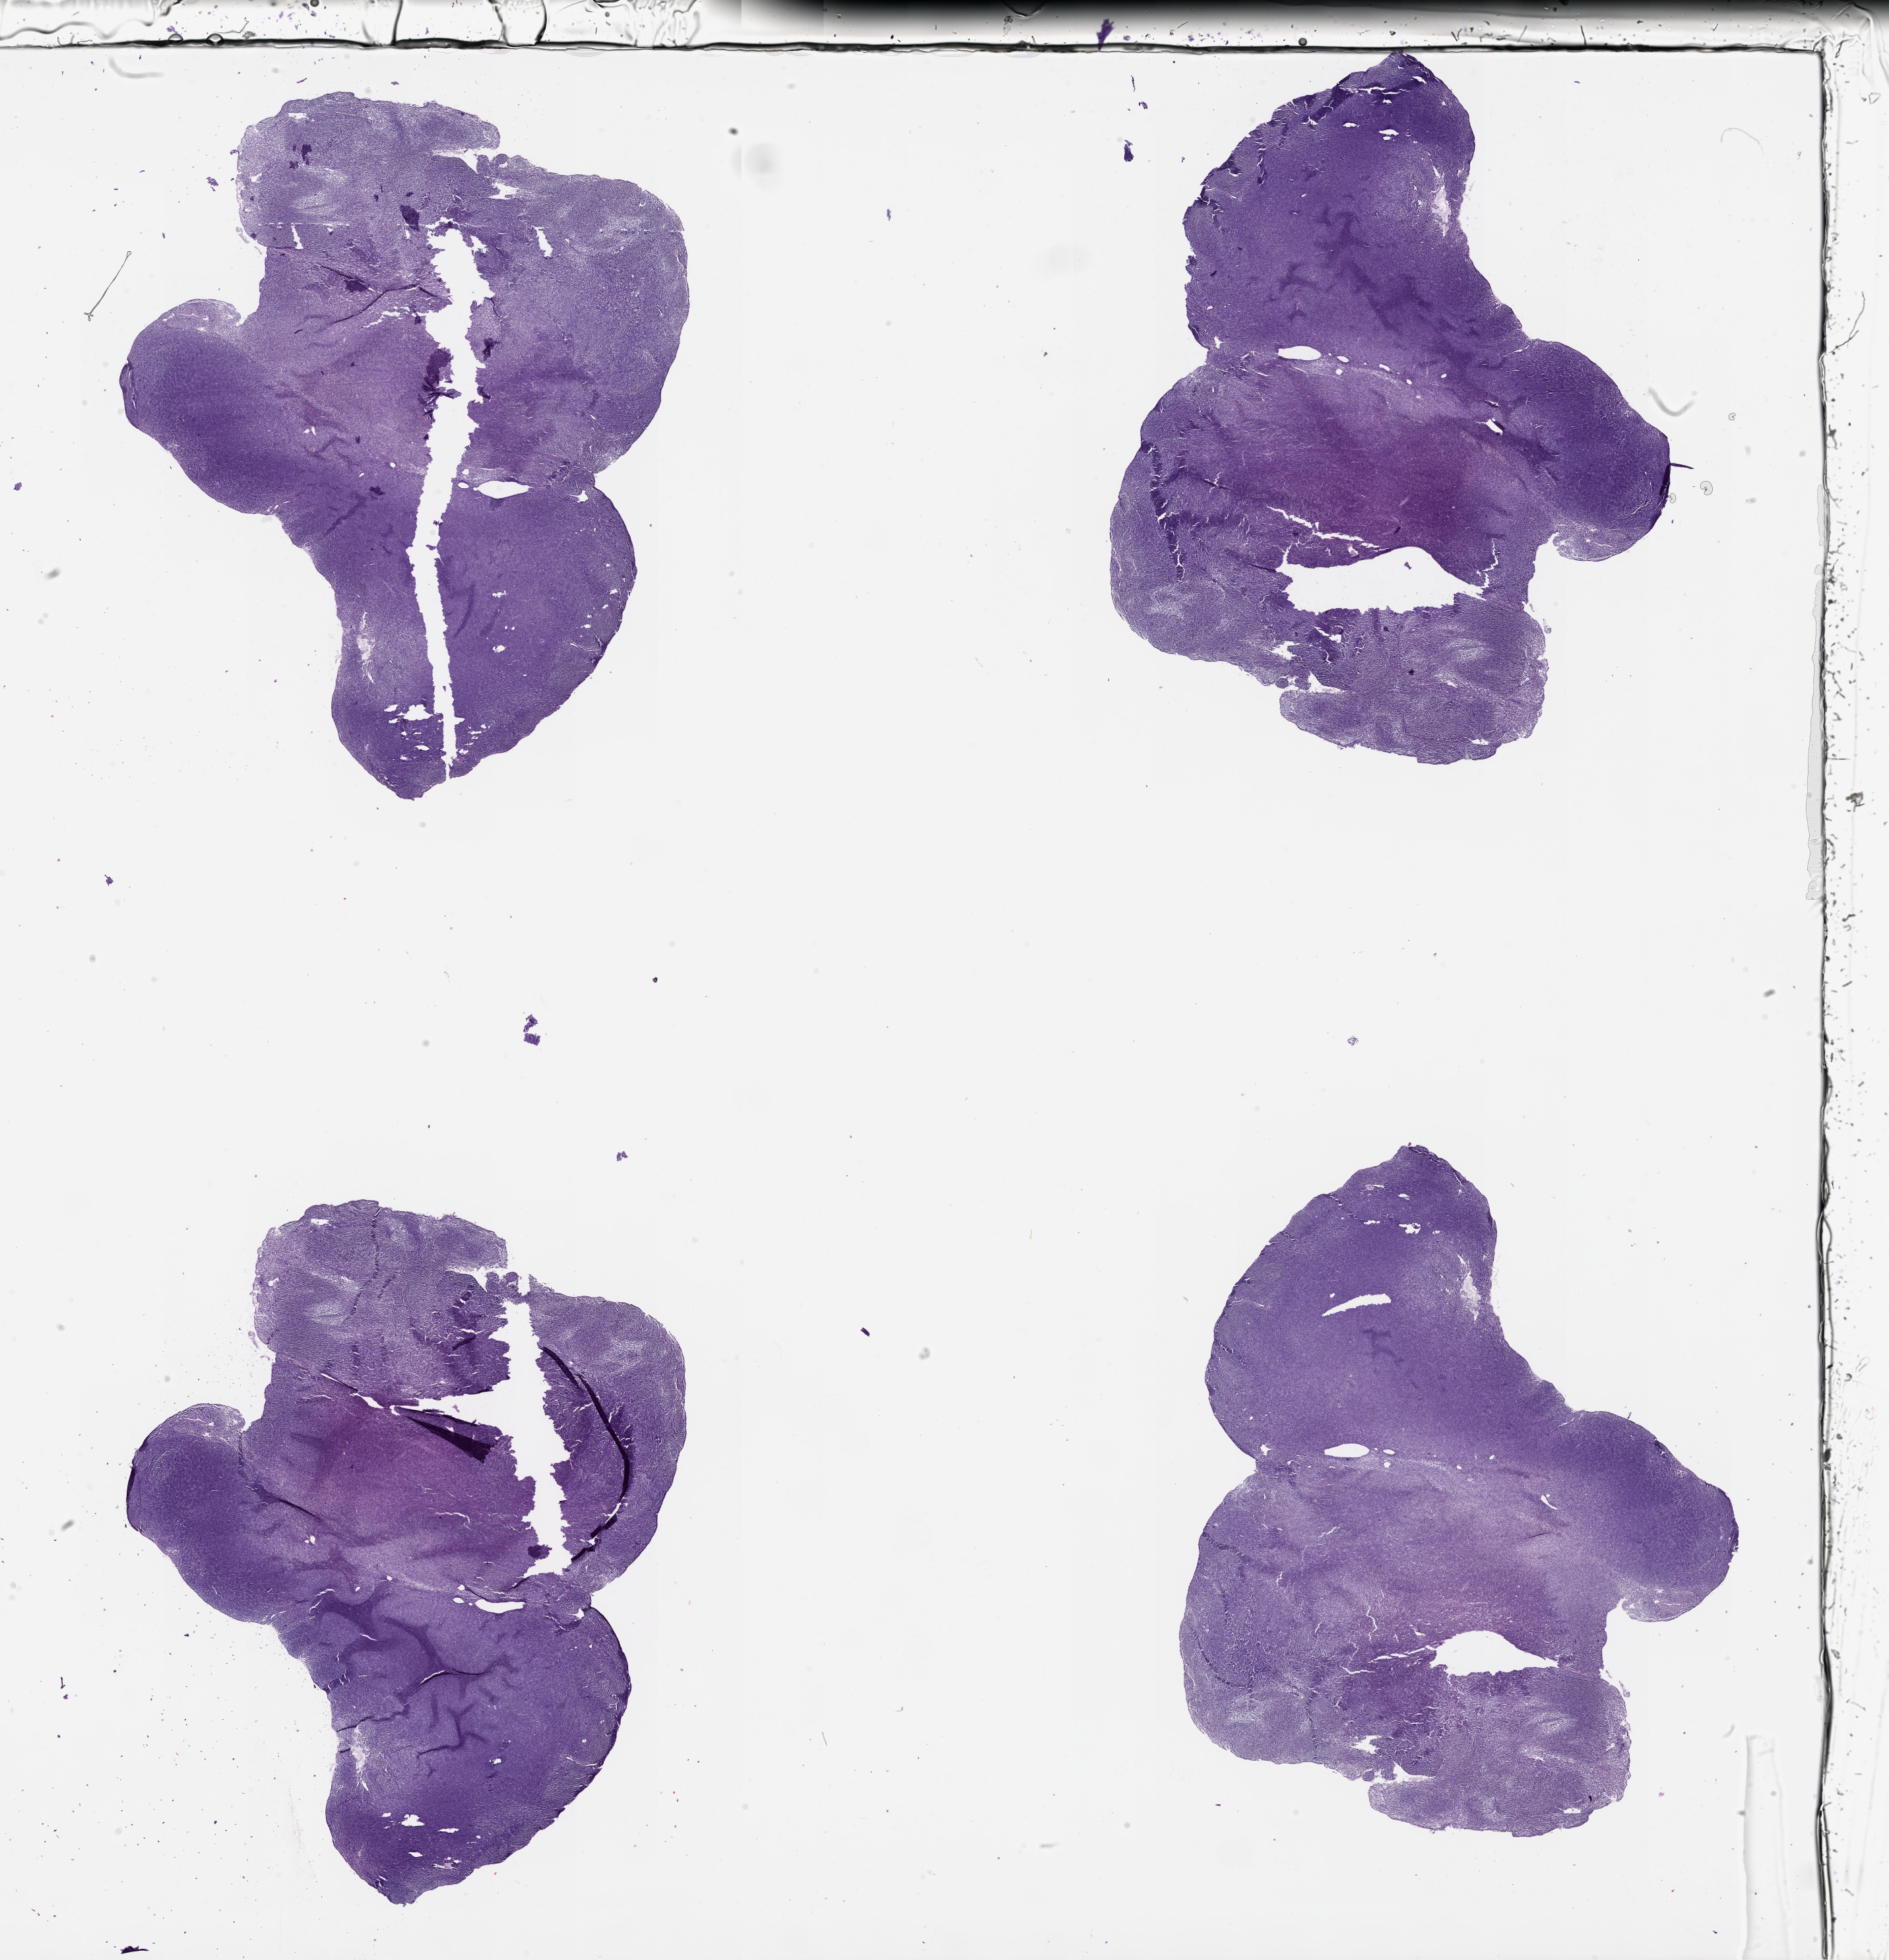
H&E whole-slide image — a low-resolution overview of the entire scanned area, about 23.1 x 23.9 mm (slide scanned at 20x).
Patient diagnosis (cohort enrolment): sarcoma (site not recorded at cohort level).